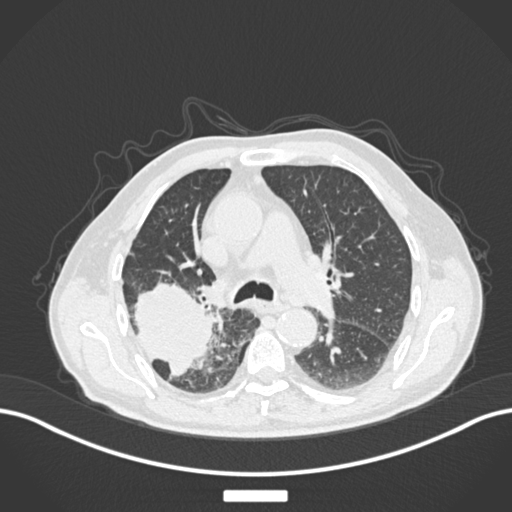
Chest CT, one axial slice. Position 111 of 201 along the scan axis. 120 kVp. Lung window (W 1500 / L -600 HU). 1 mm slice thickness. 512 × 512 image matrix, field of view 400 × 400 mm. Patient: male, 72 years. Case-level facts recorded for this patient, not image findings: clinical TNM (as recorded): T3 N2 M0.
Annotated regions visible in this slice (bounding box drawn by a radiologist):
- lung tumour (recorded histology: adenocarcinoma): box from (x=131, y=281) to (x=213, y=378) px